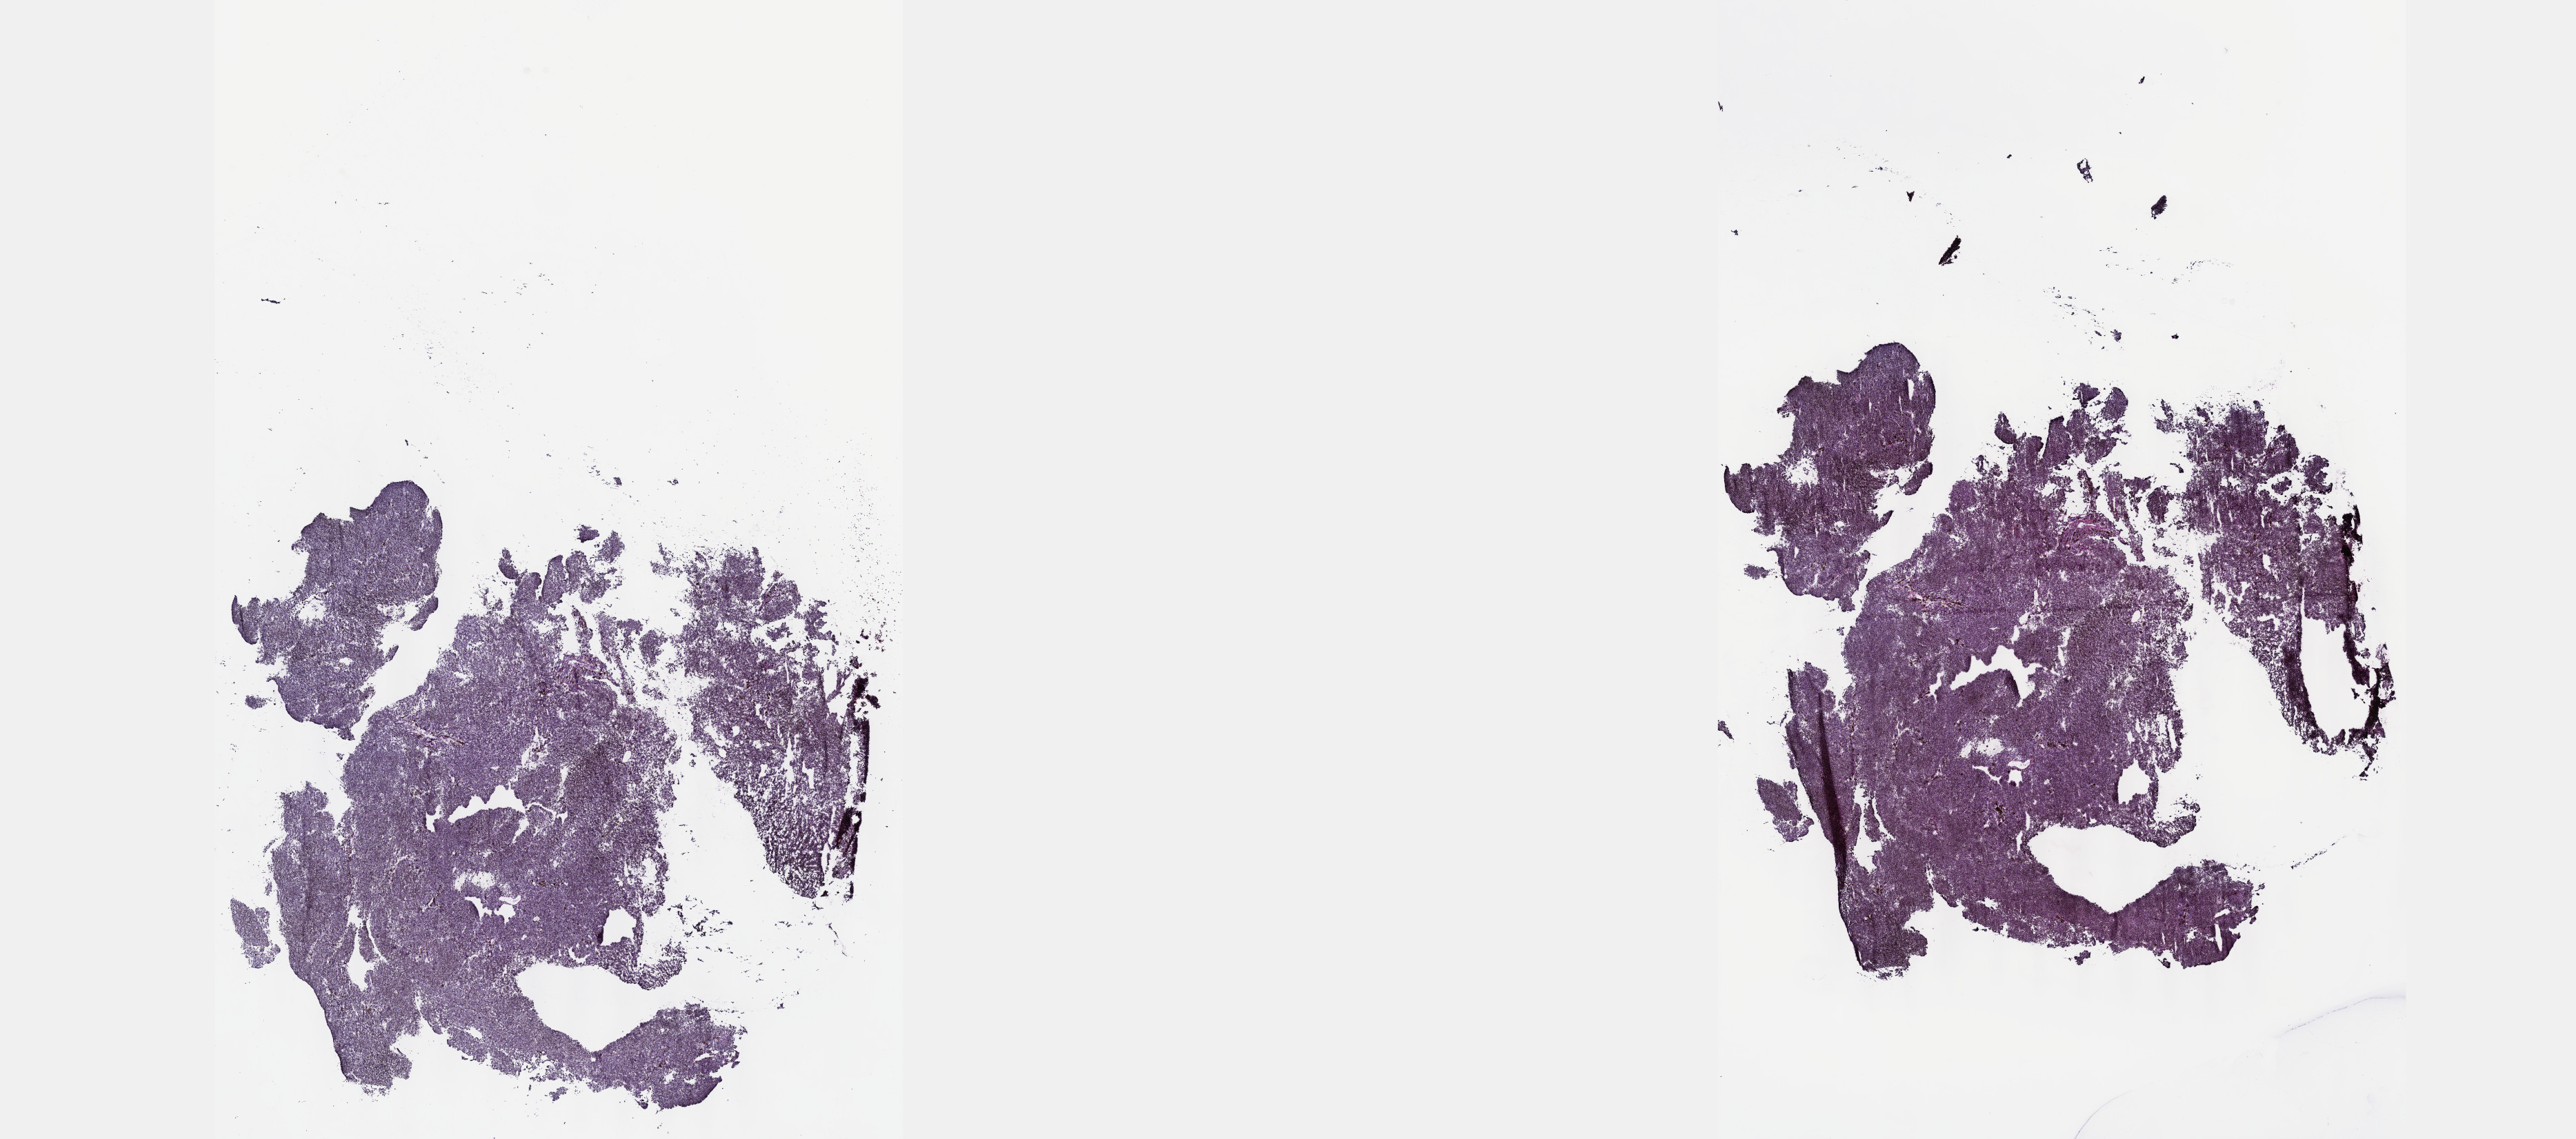
Digitized H&E tissue section (whole slide) — shown as a low-resolution overview of the whole scanned area (about 30.2 x 13.3 mm, slide scanned at 40x). Frozen section. Uvea, primary tumour sample. Male patient; age at initial diagnosis 76 years. Slide review estimates, as recorded: tumour cells 100%, tumour nuclei 80%, normal cells 0%, stromal cells 0%, necrosis 0%. Inflammatory infiltration, as recorded: lymphocyte infiltration 2%, monocyte infiltration 0%, neutrophil infiltration 0%.
AJCC pathologic stage: IIIA. TNM: T4a N0 M0. Histologic diagnosis: Epithelioid cell melanoma (choroid).